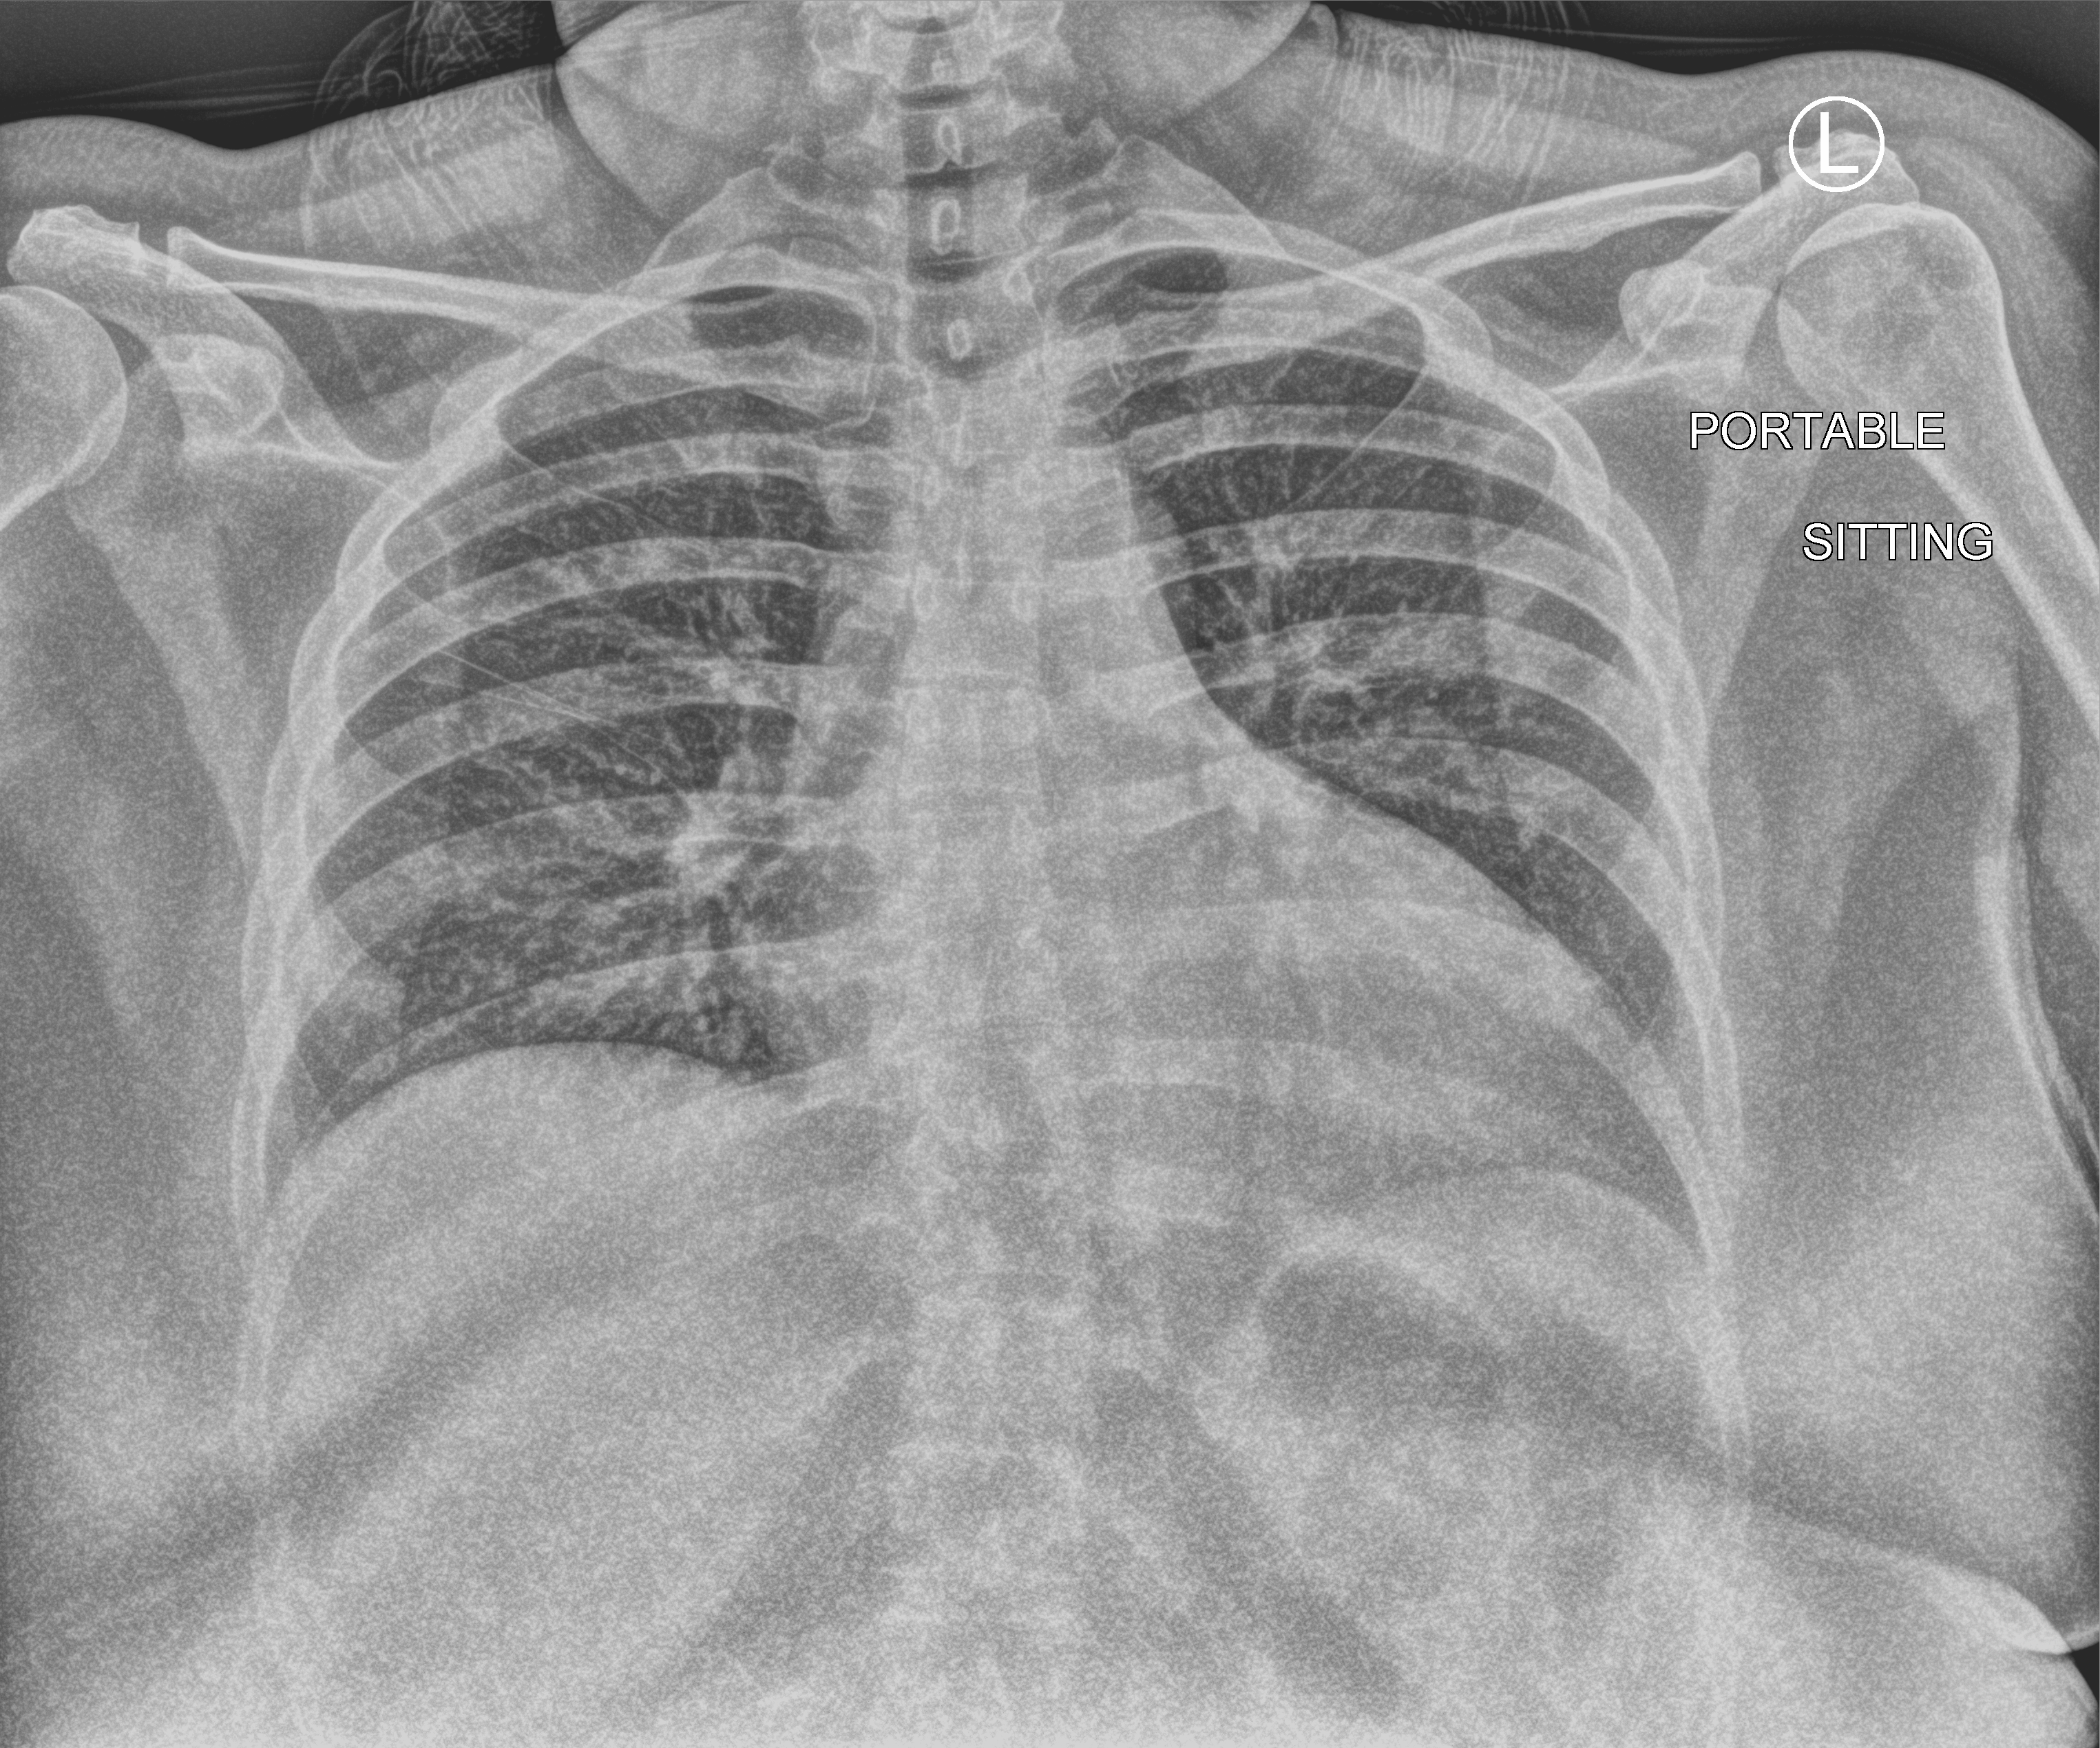
Portable chest radiograph, anteroposterior (AP) projection. Patient hospitalised with COVID-19; female, aged 18–59 years.
Admission-level facts for this patient (not findings on this image; timing relative to this image not recorded):
- chronic kidney disease (admission record): no
- mechanically ventilated during this hospital stay: no